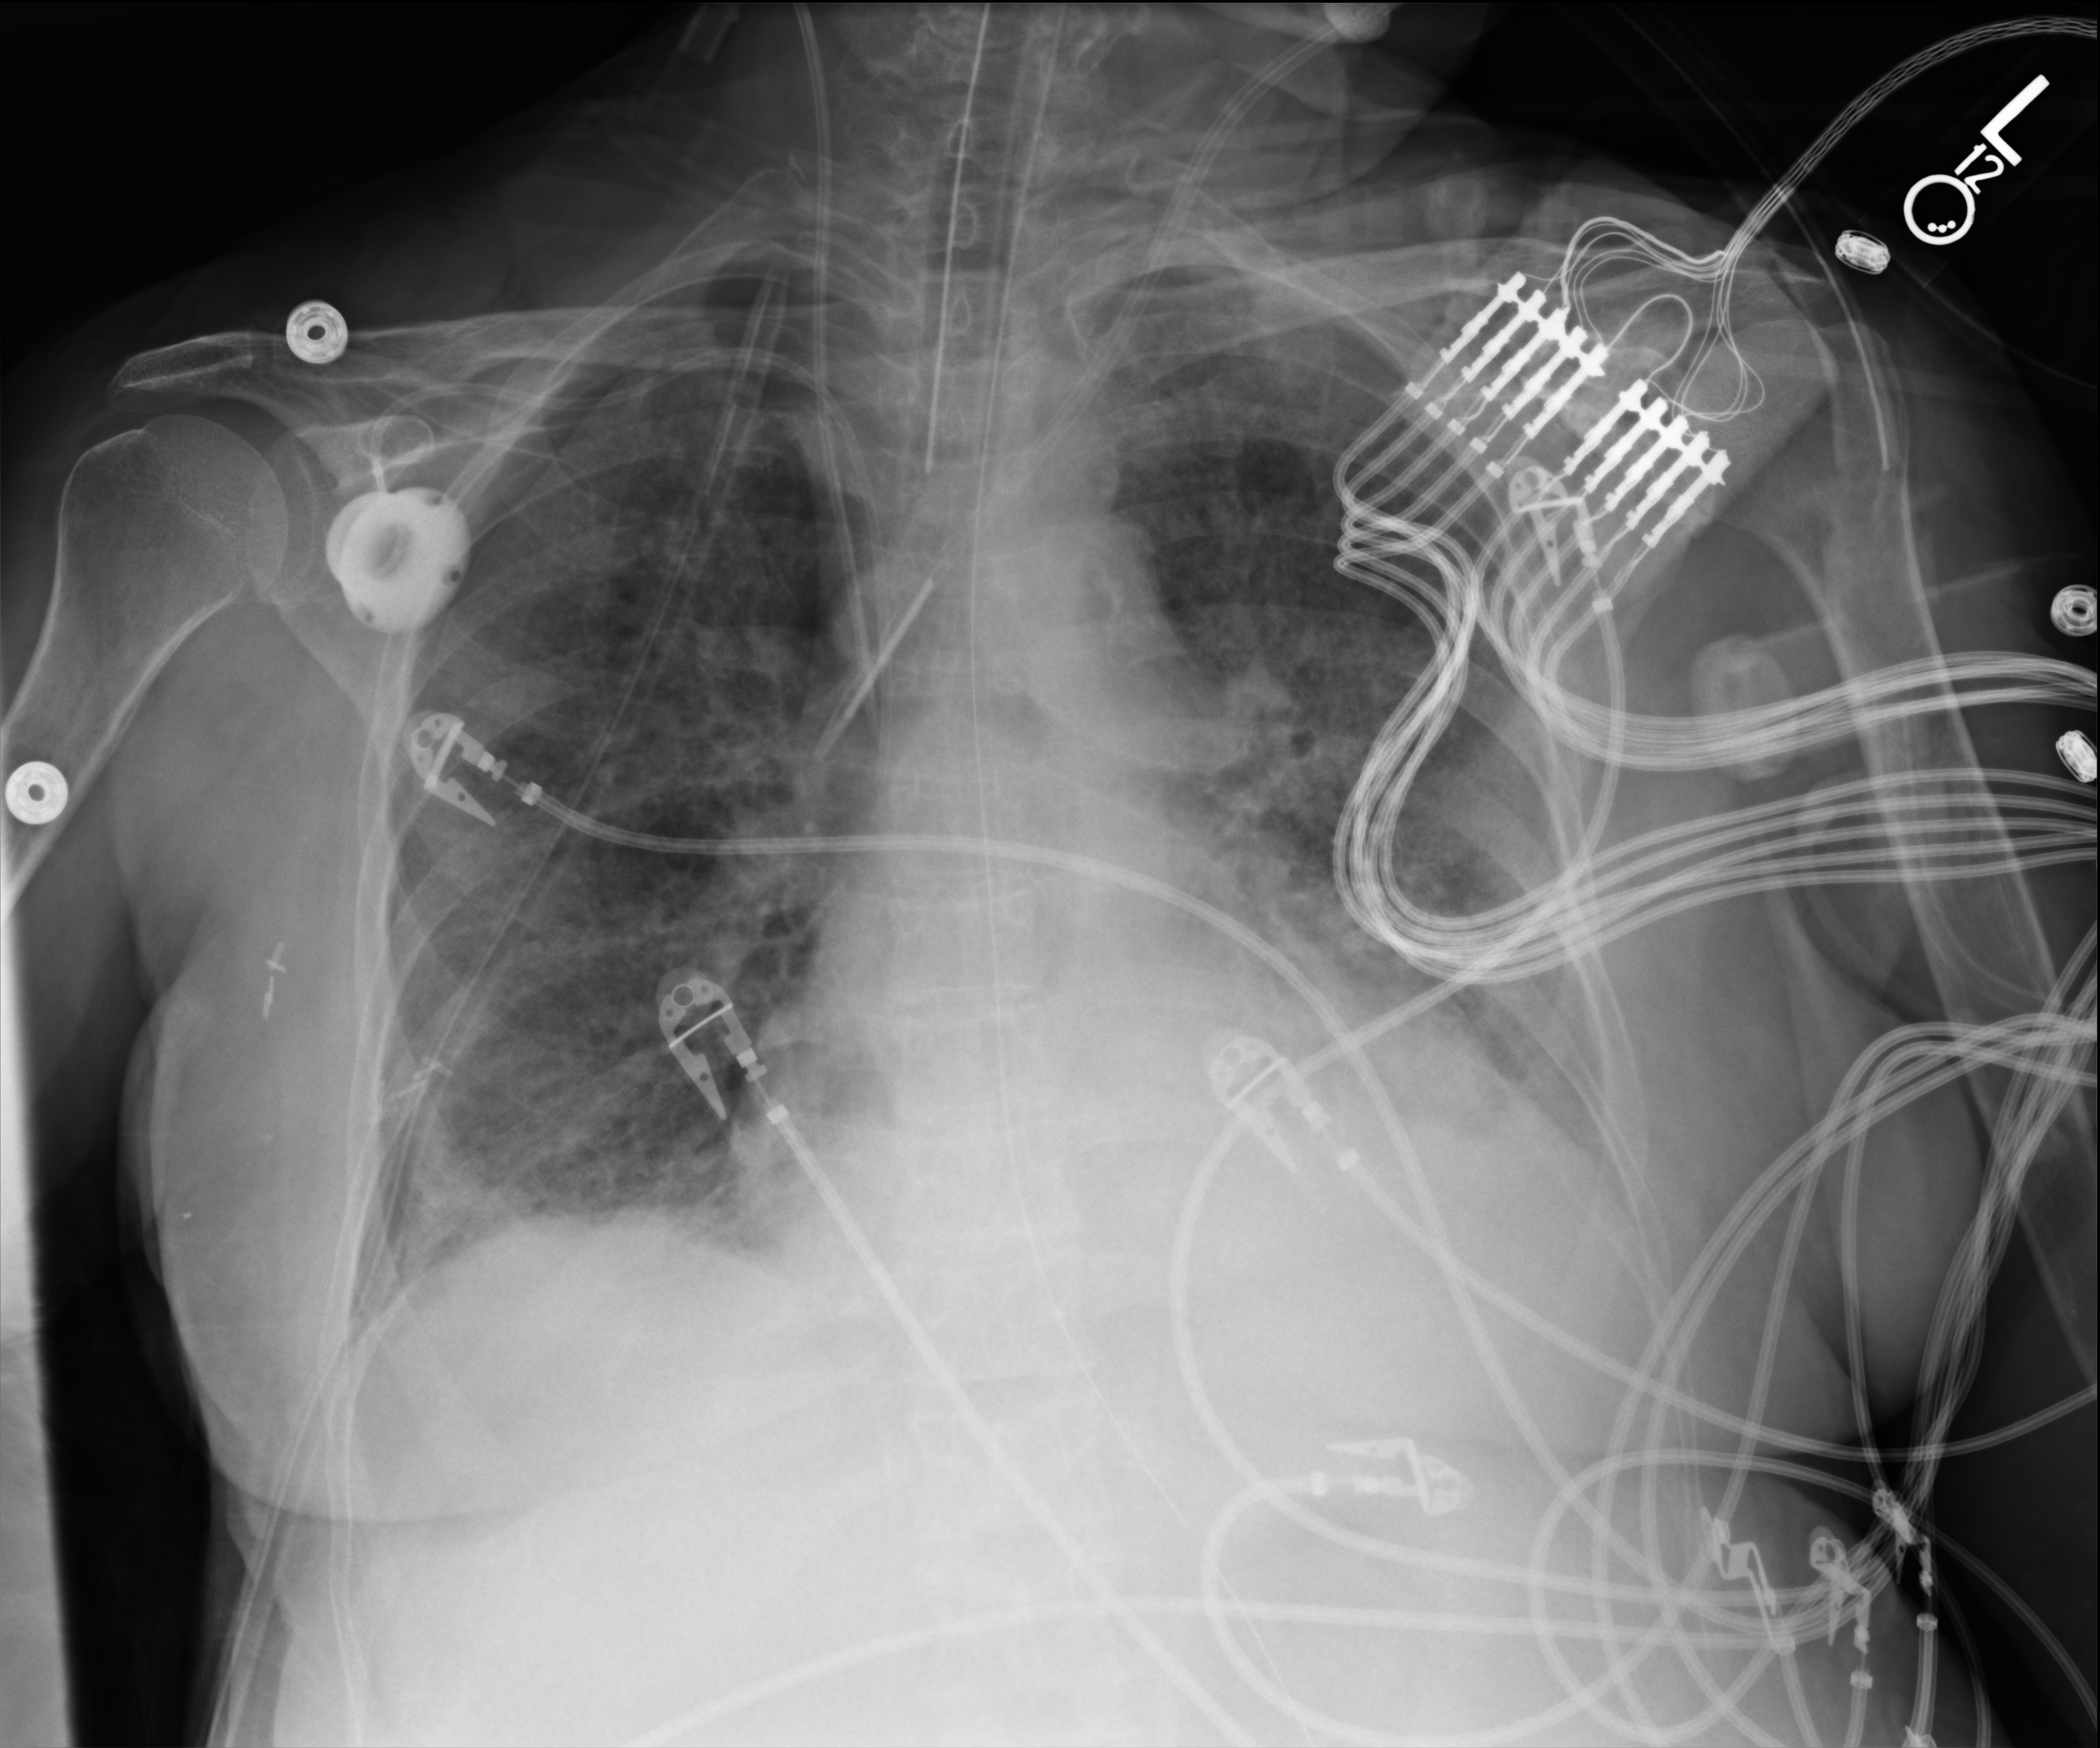
Portable chest radiograph; anteroposterior (AP) projection. Female patient hospitalised with COVID-19, age 60–74 years.
From the hospital-stay record, not from the radiograph (when in the stay this image was taken is not recorded):
- admitted to intensive care during this hospital stay: yes
- COPD (admission record): no